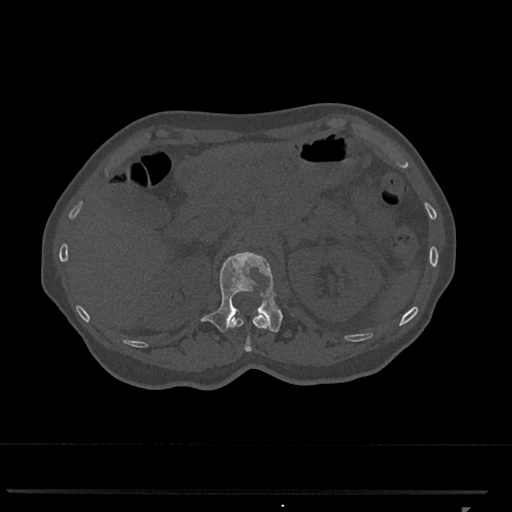
CT including the spine, one axial slice. Position 420 of 793 along the scan axis. Bone window (W 1800 / L 400 HU). 512 × 512 image matrix, field of view 380 × 380 mm. Female patient, age 62 years. From the clinical record (not read from this slice): primary cancer: renal.
Outlined on this slice (semi-automatic segmentation, software-assisted and operator-edited):
- L1 vertebra: box from (x=200, y=252) to (x=294, y=333) px
- T12 vertebra: (x=229, y=313)–(x=267, y=351)